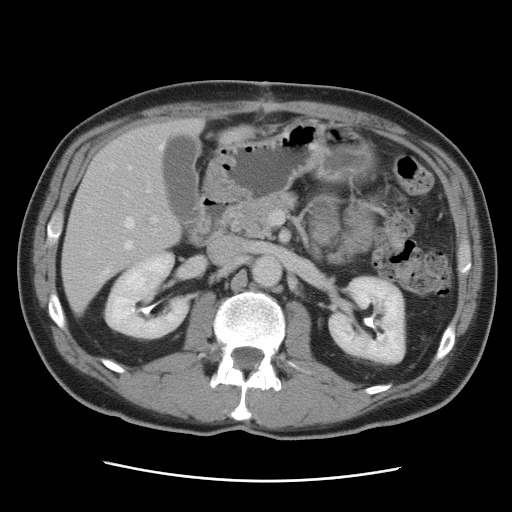
Contrast-enhanced abdominal CT, one axial slice. Slice 43 of 89 in the series (ordered by position). 120 kVp. Intravenous contrast given. Soft-tissue window (W 400 / L 40 HU). 5 mm slice thickness. 512 × 512 image matrix, field of view 366 × 366 mm. Male patient, age 59 years. From the clinical record (not read from this slice): diagnosis: colorectal cancer liver metastases, imaged before liver resection; multiple liver metastases: yes; largest metastasis: 0.6 cm; disease in both lobes: yes.
Annotated regions visible in this slice (manually delineated by an expert):
- hepatic veins: bounding box (x1, y1, x2, y2) in pixels: (89, 145, 164, 280)
- liver: (64, 119, 251, 316)
- planned liver remnant (the part of the liver to remain after resection): (72, 119, 202, 245)
- portal vein (with intrahepatic branches): (126, 188, 157, 223)